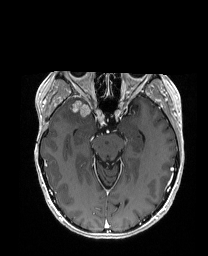
Brain MRI from a brain-tumour surgery series, one axial slice. Slice 112 of 192 in the series (ordered by position). T1-weighted post-contrast. 208 × 256 image matrix, field of view 203 × 250 mm. Case-level facts recorded for this patient, not image findings: histopathology: Metastatic Carcinoma from Breast primary; tumour location: Right Frontal.
Annotated regions visible in this slice (outlined manually by an expert reader):
- tumour: box from (x=69, y=99) to (x=88, y=114) px